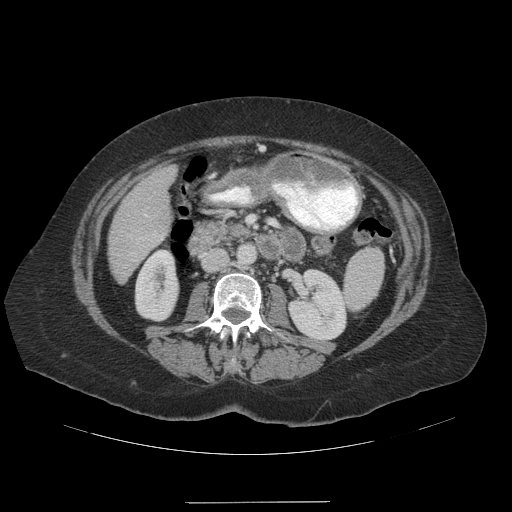
Contrast-enhanced abdominal CT (liver protocol), one axial slice. Slice 42 of 99 in the series (ordered by position). Reconstruction kernel STANDARD. Soft-tissue window (W 400 / L 40 HU). 512 × 512 image matrix, field of view 440 × 440 mm. From the clinical record (not read from this slice): diagnosis: hepatocellular carcinoma (patient treated with transarterial chemoembolisation; whether this scan precedes or follows treatment is not stated here); TNM stage (as recorded): Stage-IVA; Child-Pugh class: A; tumour nodularity: multinodular.
Annotated regions visible in this slice (semi-automatic segmentation, software-assisted and operator-edited):
- liver parenchyma outside the tumour (the mass and vessels are separate outlines, so this box may not span the whole liver): bounding box <108,166,176,282> (left, top, right, bottom; pixels)
- liver vessels: <132,214,148,254>